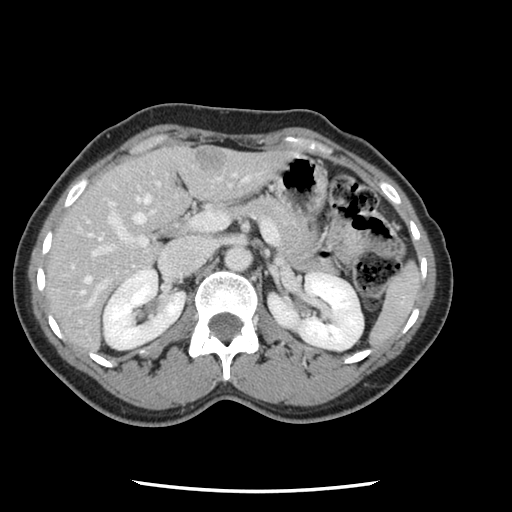
Contrast-enhanced abdominal CT, one axial slice. Slice 64 of 134 in the series (ordered by position). Intravenous contrast given. Soft-tissue window (W 400 / L 40 HU). 2.5 mm slice thickness. 512 × 512 image matrix. Female patient, age 43 years. Case-level facts recorded for this patient, not image findings: diagnosis: colorectal cancer liver metastases, imaged before liver resection; multiple liver metastases: yes; largest metastasis: 3.4 cm; chemotherapy before resection: no.
Outlined on this slice (outlined manually by an expert reader):
- hepatic veins: bounding box (x1, y1, x2, y2) in pixels: (81, 179, 246, 294)
- liver: (45, 144, 290, 351)
- planned liver remnant (the part of the liver to remain after resection): (46, 150, 185, 308)
- portal vein (with intrahepatic branches): (82, 174, 278, 310)
- liver metastasis: (194, 152, 228, 173)